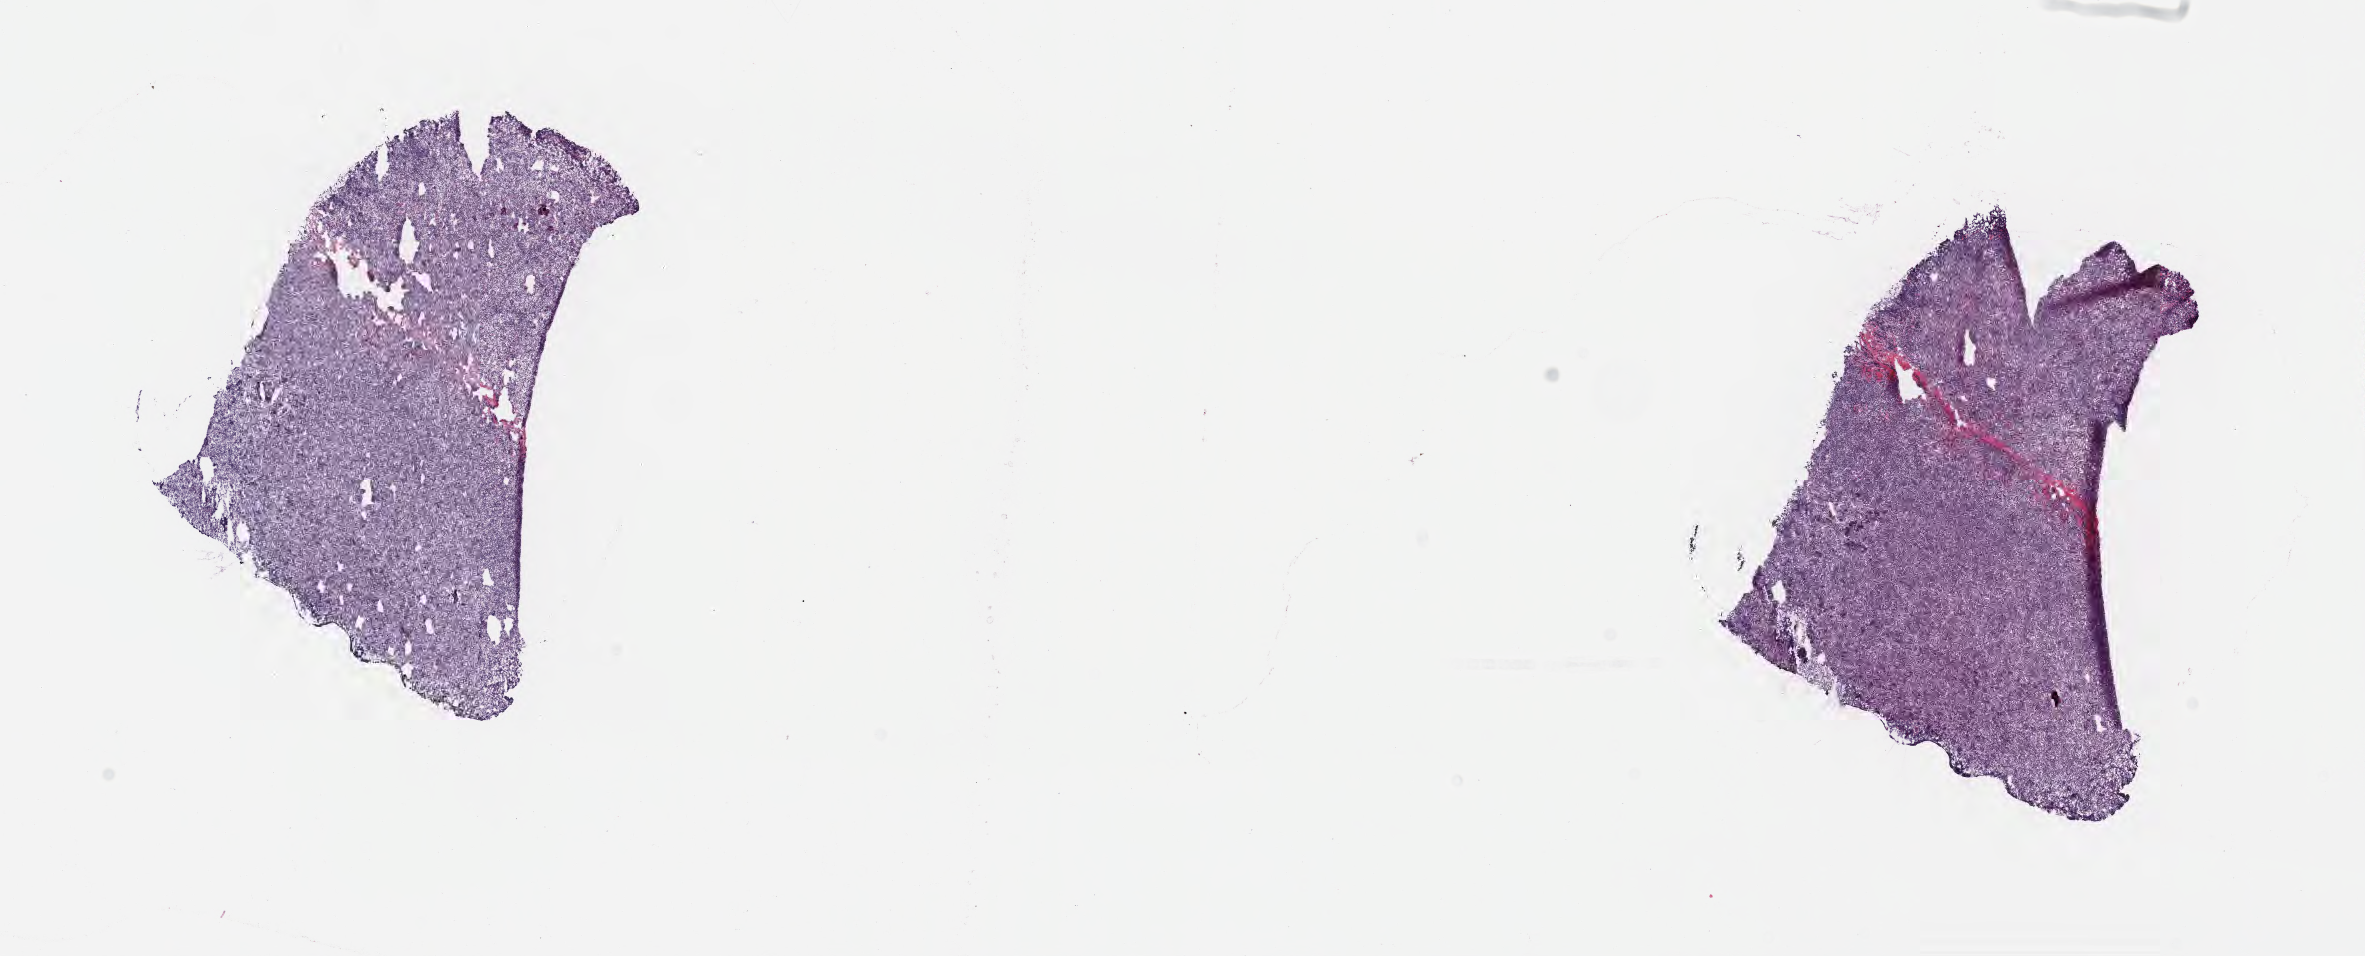
Hematoxylin and eosin (H&E) whole-slide image — whole scanned area (about 19.1 x 7.7 mm) shown as a low-resolution overview; cryosection; primary tumor; site: cranium. Male patient; age at initial diagnosis 2 years. Slide review estimates, as recorded: tumor cells 90%, tumor nuclei 90%, stromal cells 5%, necrosis 0%, normal cells 5%. Inflammatory infiltration, as recorded: lymphocyte infiltration 40%, monocyte infiltration 35%, neutrophil infiltration 5%.
• diagnosis: Burkitt lymphoma, NOS
• Ann Arbor stage (patient): Stage IV
• section: bottom of the tissue portion